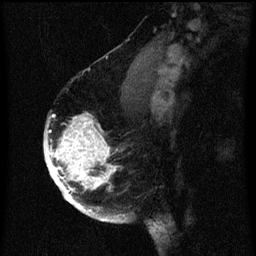
Breast MRI (dynamic contrast-enhanced), one sagittal slice. Slice 43 of 60 in the series (ordered by position). Dynamic contrast-enhanced series, image 2 of 3 at this slice position (ordered by acquisition). 1.5 T. TE 4.2 ms, TR 8 ms. 2 mm slice thickness. 256 × 256 image matrix, field of view 180 × 180 mm. Female patient, age 56 years.
Outlined on this slice (semi-automatic segmentation, software-assisted and operator-edited):
- analysis volume of interest (the breast-tissue region the enhancement analysis was run in; not a lesion): bounding box <46,116,125,219> (left, top, right, bottom; pixels)
- tumour enhancement mask (voxels above the 70 % enhancement threshold inside the analysis volume of interest): <46,116,125,219>